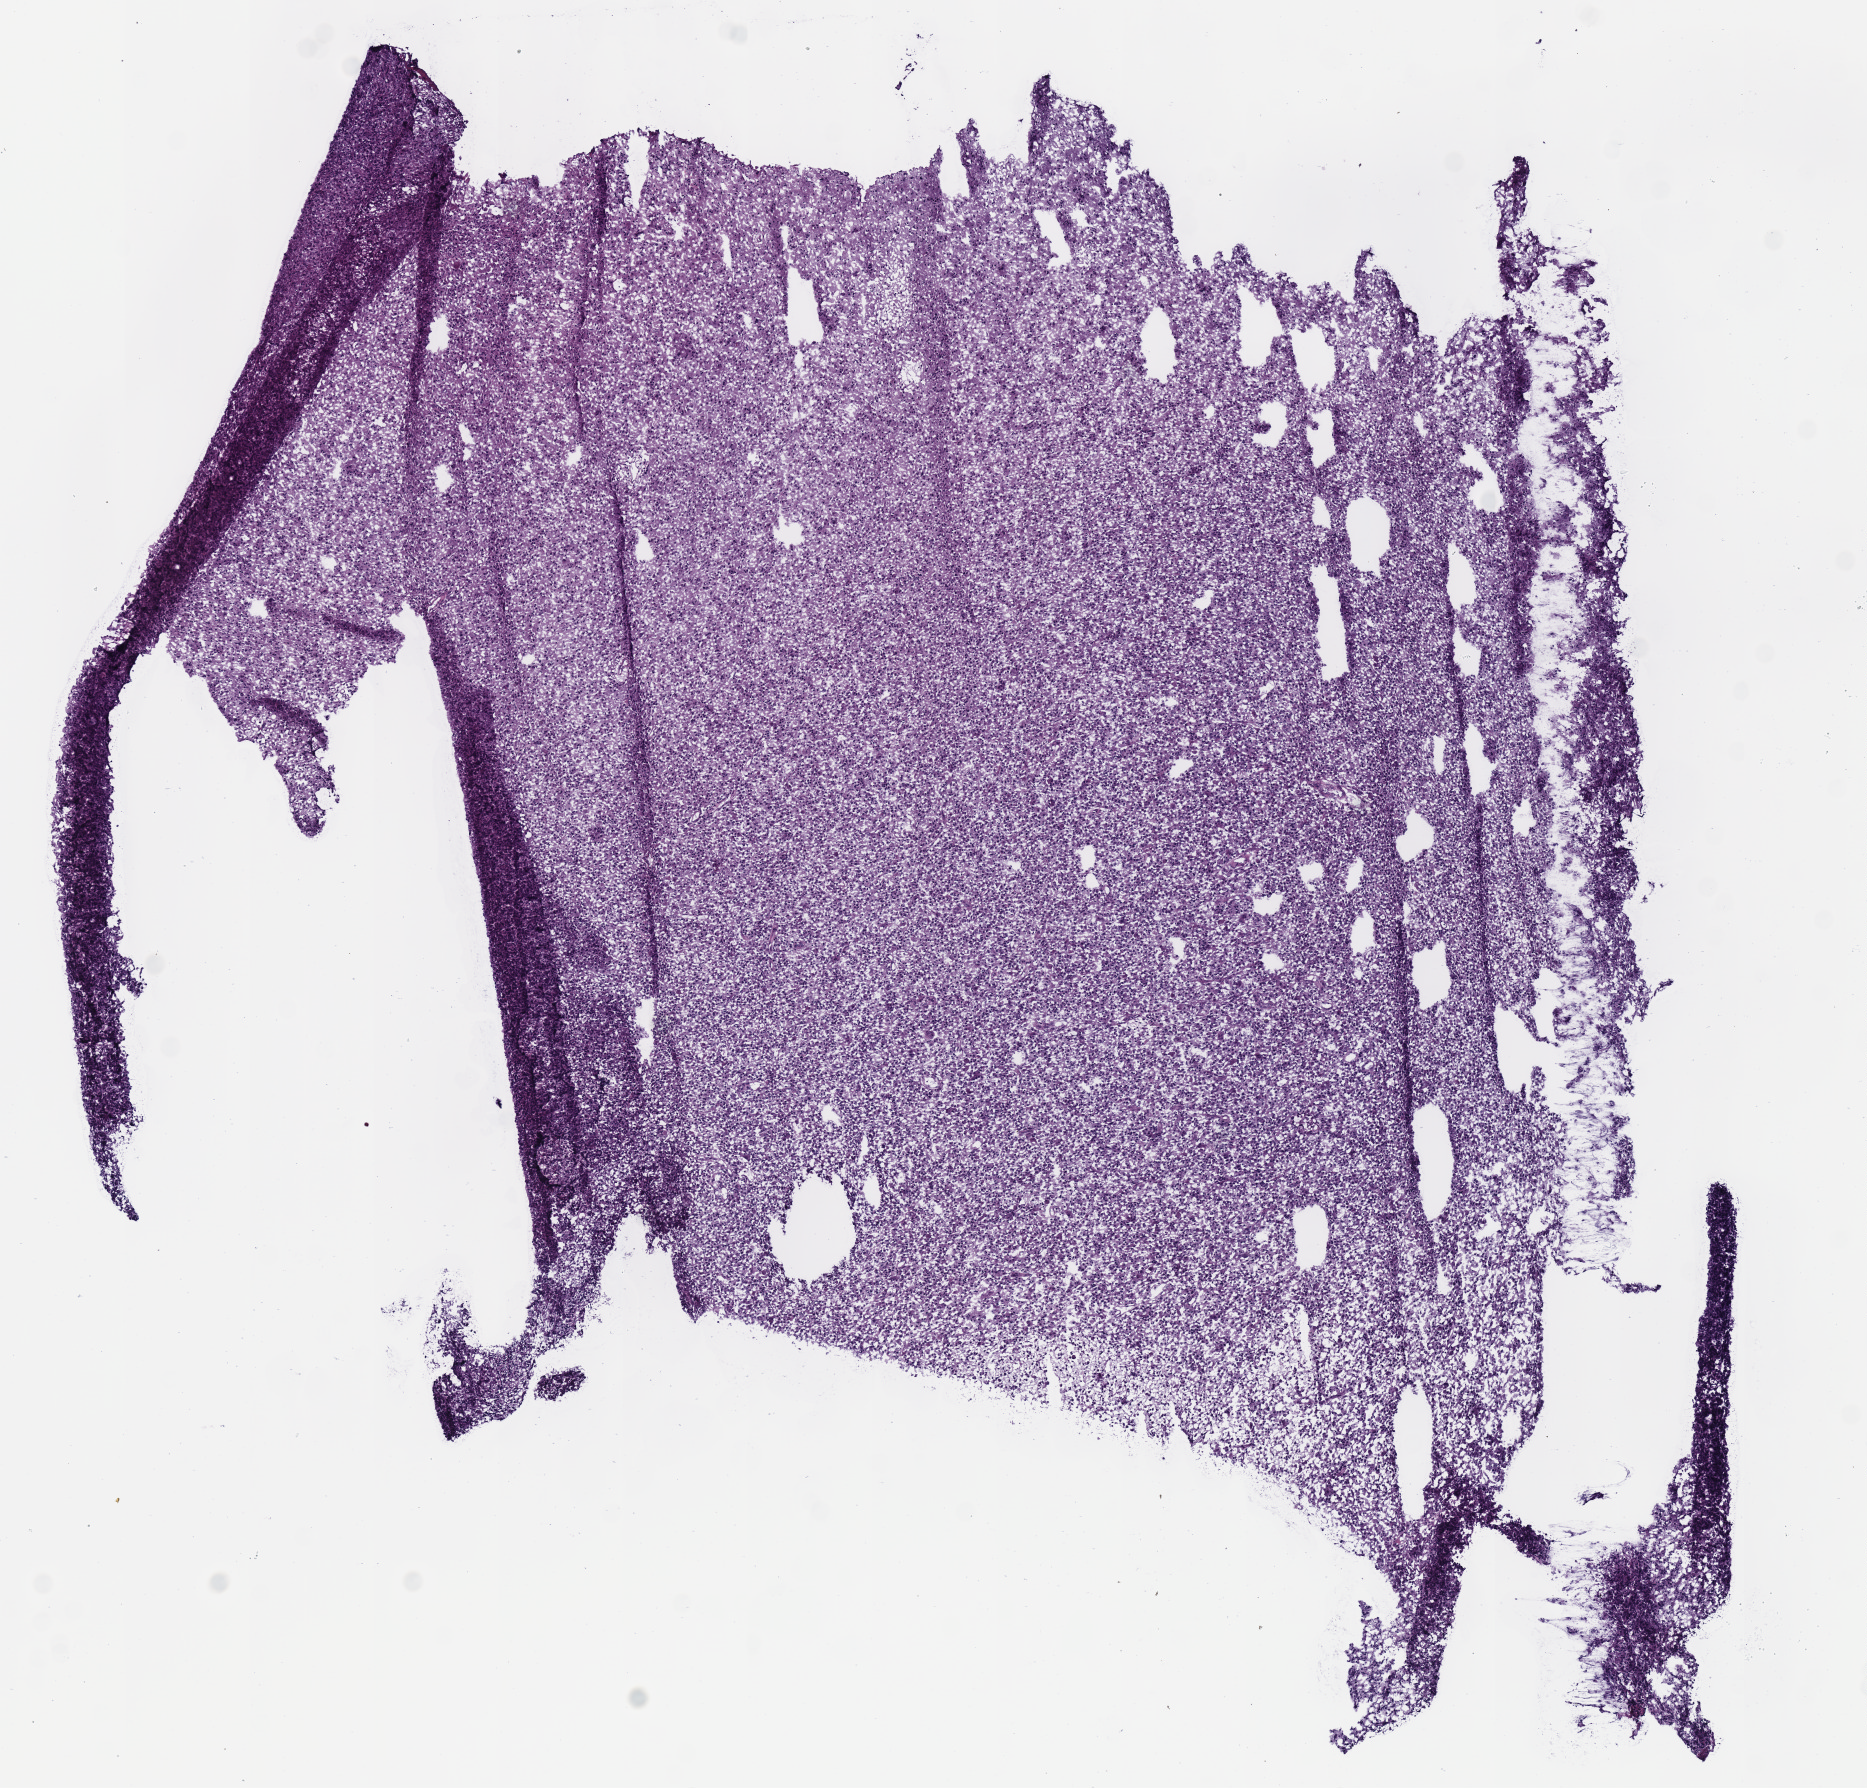
Digitized H&E-stained tissue section (whole slide) — a low-resolution overview of the entire scanned area, about 7.3 x 7.0 mm (from a 40x scan); frozen section from the top of the tissue portion; primary tumour sample from the brain. Patient: male, age at initial diagnosis 55 years. Histologic grade: G3 (poorly differentiated). Pathologist review of this section (percent, as recorded): tumour cells 100%, tumour nuclei 80%, normal cells 0%, stromal cells 0%, necrosis 0%.
Diagnosis: Astrocytoma, anaplastic (cerebrum).